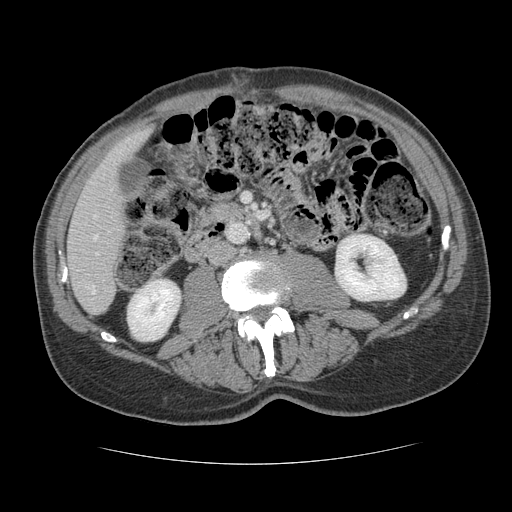
Contrast-enhanced abdominal CT, one axial slice. Position 40 of 134 along the scan axis. Reconstruction kernel STANDARD. 120 kVp. Soft-tissue window (W 400 / L 40 HU). 512 × 512 image matrix. Male patient, age 68 years. From the clinical record (not read from this slice): diagnosis: colorectal cancer liver metastases, imaged before liver resection; multiple liver metastases: yes; largest metastasis: 2.2 cm; disease in both lobes: no.
Outlined on this slice (manually delineated by an expert):
- hepatic veins: bounding box [x1, y1, x2, y2] px = [94, 216, 97, 239]
- liver: [68, 130, 148, 314]
- planned liver remnant (the part of the liver to remain after resection): [68, 131, 148, 314]
- portal vein (with intrahepatic branches): [92, 253, 98, 293]